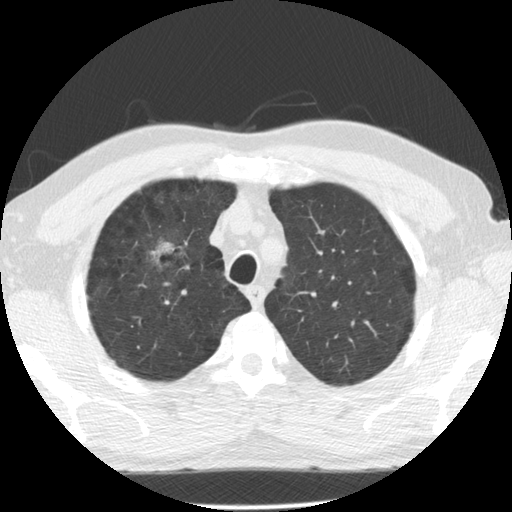
Axial slice from a low-dose chest CT screening exam. Second annual screen. Lung window (W 1500 / L -600 HU). Standard (soft-tissue) reconstruction kernel (STANDARD). 140 kVp. Slice 104 of 135 in the series. 512 × 512 image matrix. Male, age 60 years at enrolment. Former smoker at enrolment.
- Lesion marked by an expert reader, box from (x=134, y=231) to (x=190, y=289) px.
- The exam's reader record, not a measurement of the box and not confirmed to be the same lesion: non-calcified nodule or mass ≥4 mm, right upper lobe, poorly defined margins, mixed attenuation, pre-existing on the prior screen: yes; interval growth: yes.